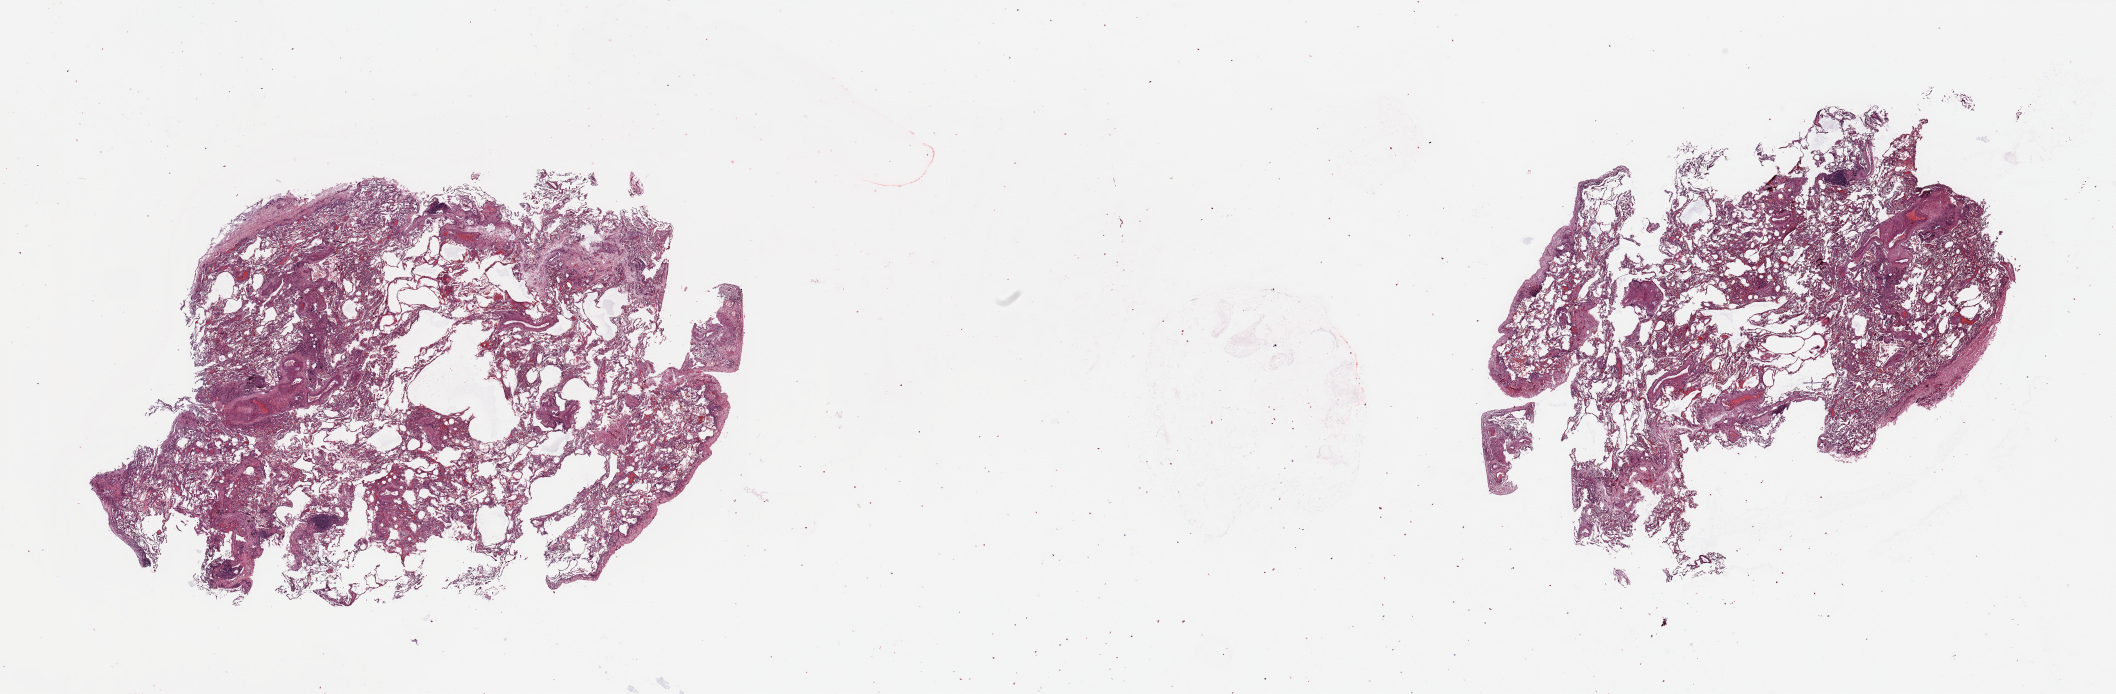
H&E whole-slide image — shown as a low-resolution overview of the whole scanned area (about 33.5 x 11.0 mm, slide scanned at 20x). Normal (non-tumour) tissue sample, lung. Patient: male, age 72 years.
This section: normal (non-tumour) tissue from the same patient. Patient diagnosis: Adenocarcinoma, NOS.